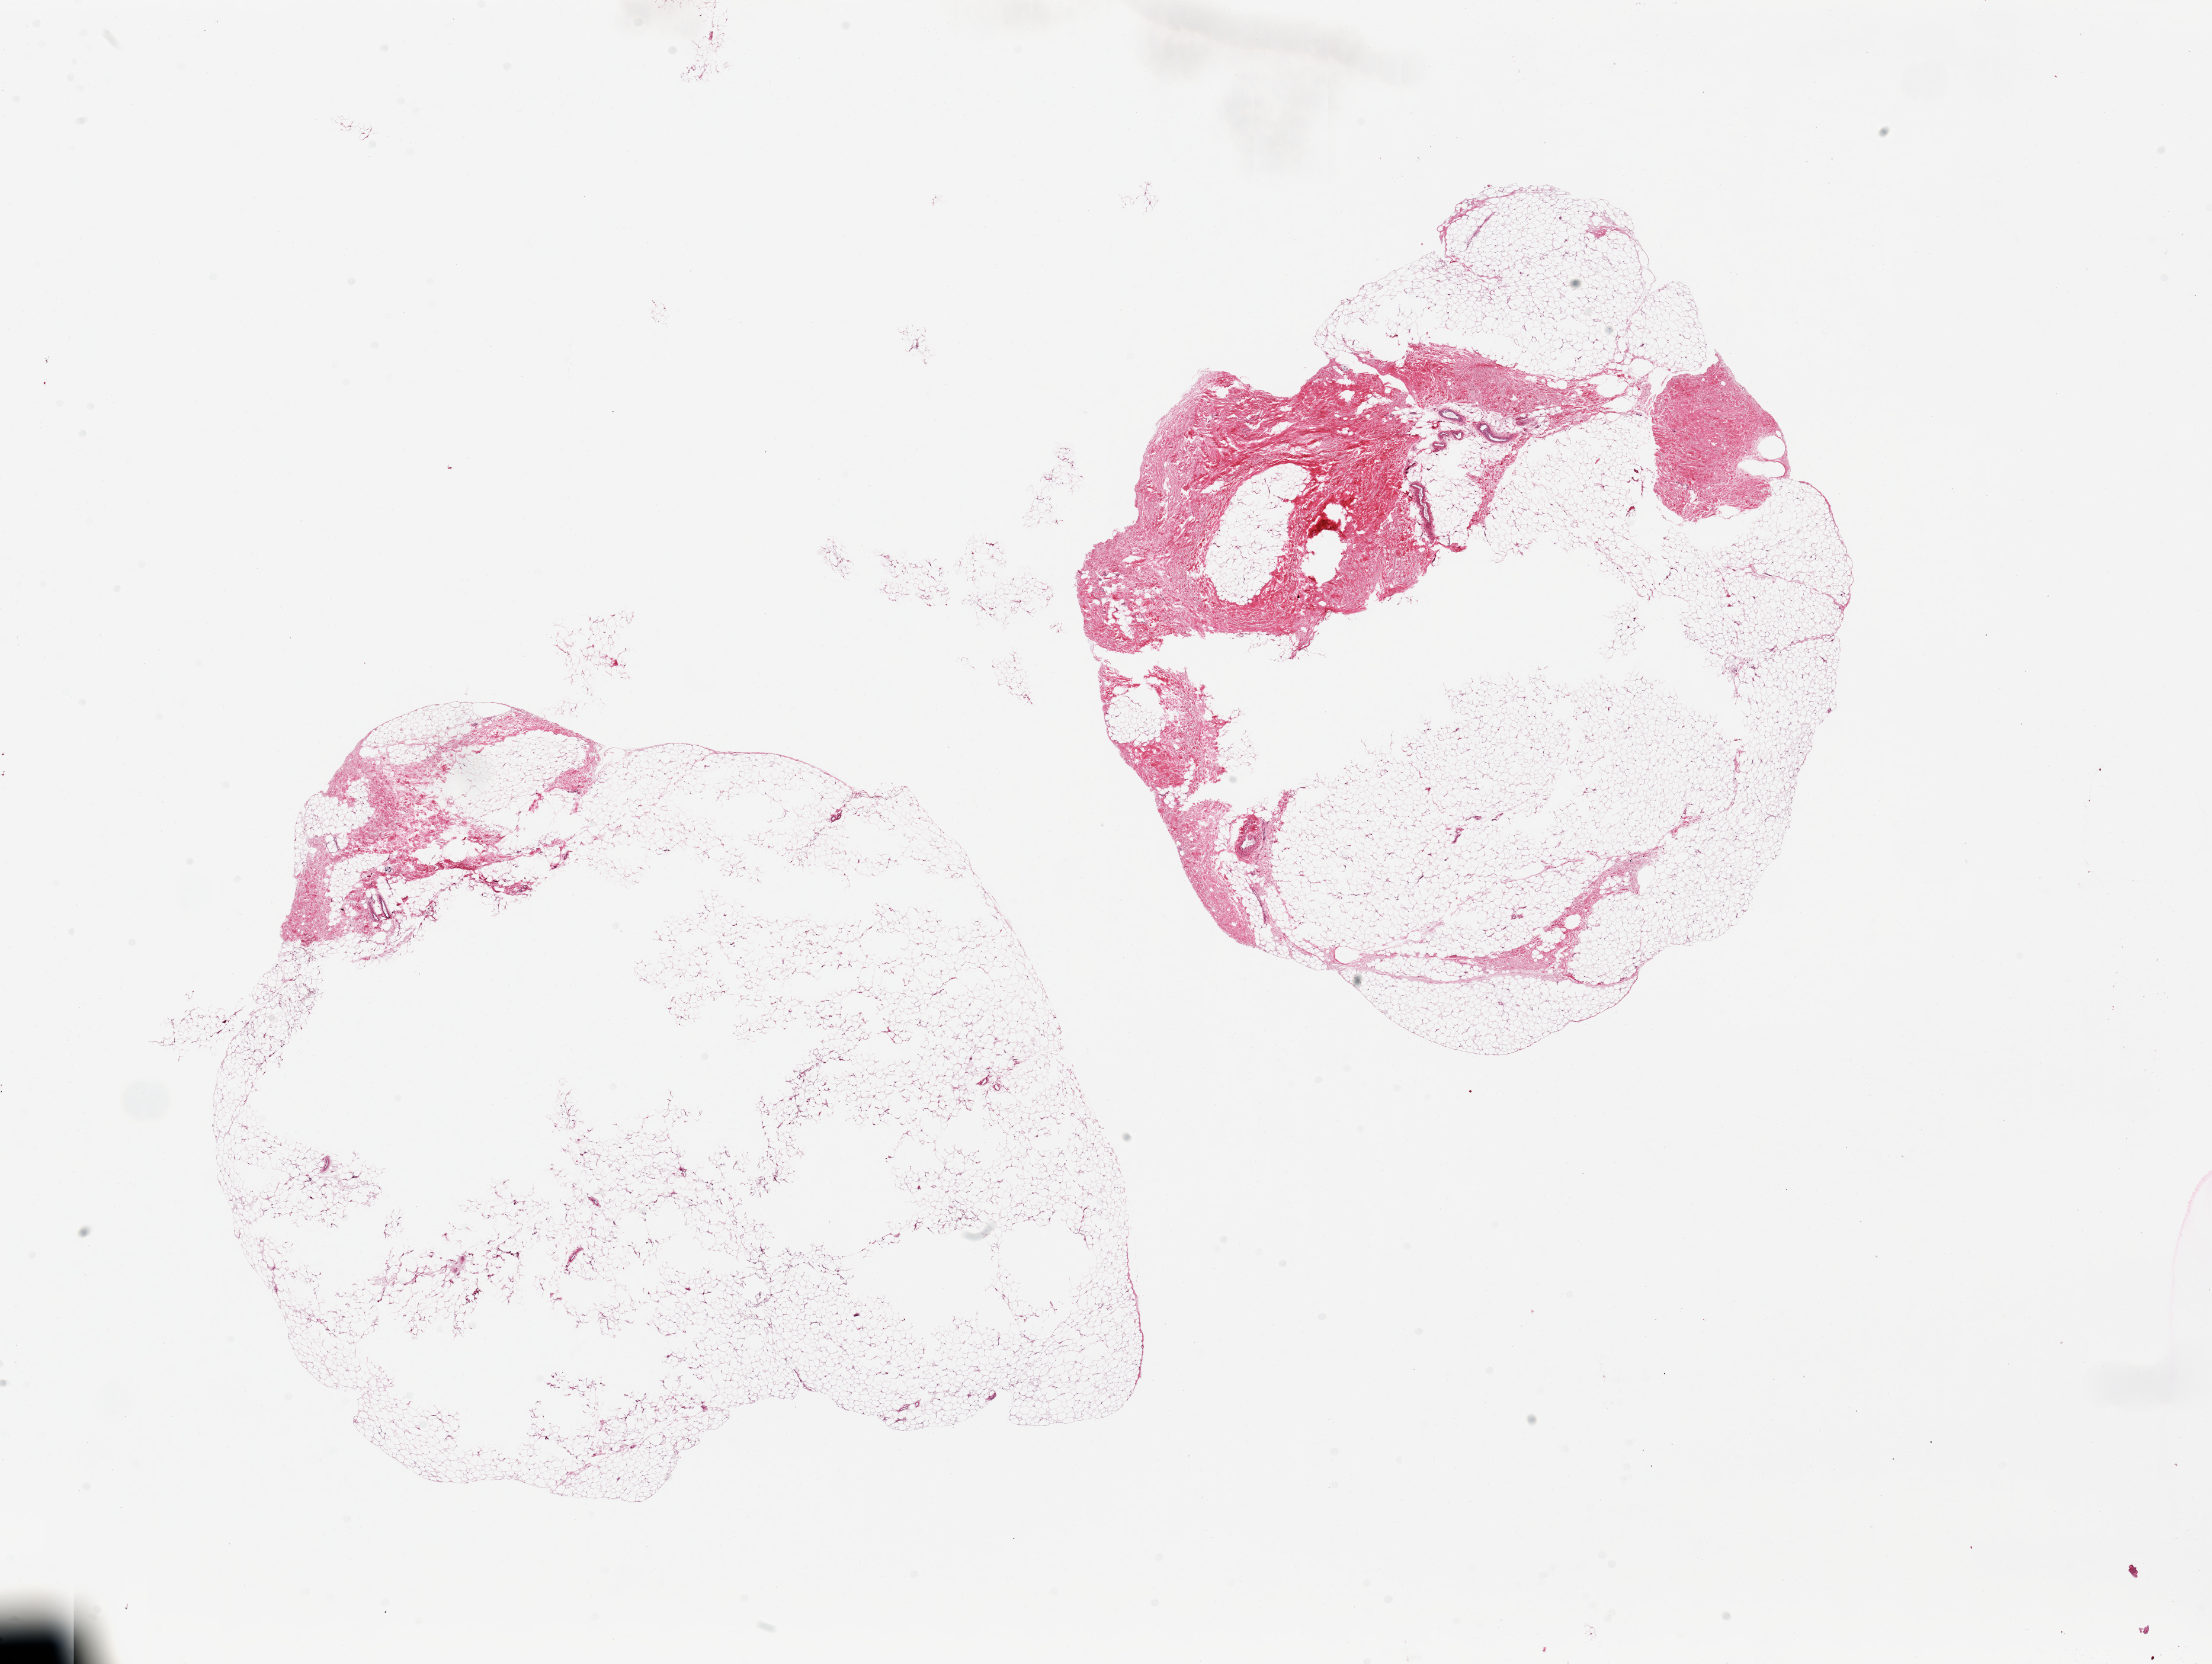
Digitized haematoxylin and eosin-stained section, shown as a low-resolution overview of the whole scanned area (about 29.5 x 22.2 mm); PAXgene-fixed, paraffin-embedded tissue; target tissue: breast; donor tissue sample.
Review note (as recorded): 2 pieces, 13x11 & 12x10.5mm; mainly fat, ~10% fibrous tissue; No TDLU.